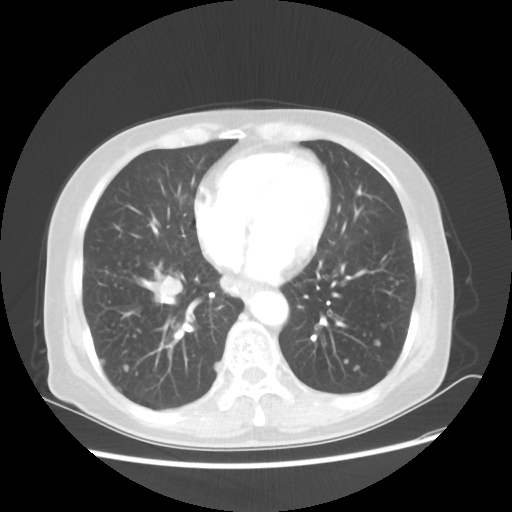
Chest CT, one axial slice. Slice 20 of 56 in the series (ordered by position). 80 kVp. Lung window (W 1500 / L -600 HU). 5 mm slice thickness. 512 × 512 image matrix, field of view 360 × 360 mm. Patient: female, 68 years. Case-level facts recorded for this patient, not image findings: clinical TNM (as recorded): T1c N3 M0.
Structures marked on this image (rectangle marked by the reading radiologist):
- lung tumour (recorded histology: squamous cell carcinoma): box from (x=153, y=262) to (x=191, y=312) px